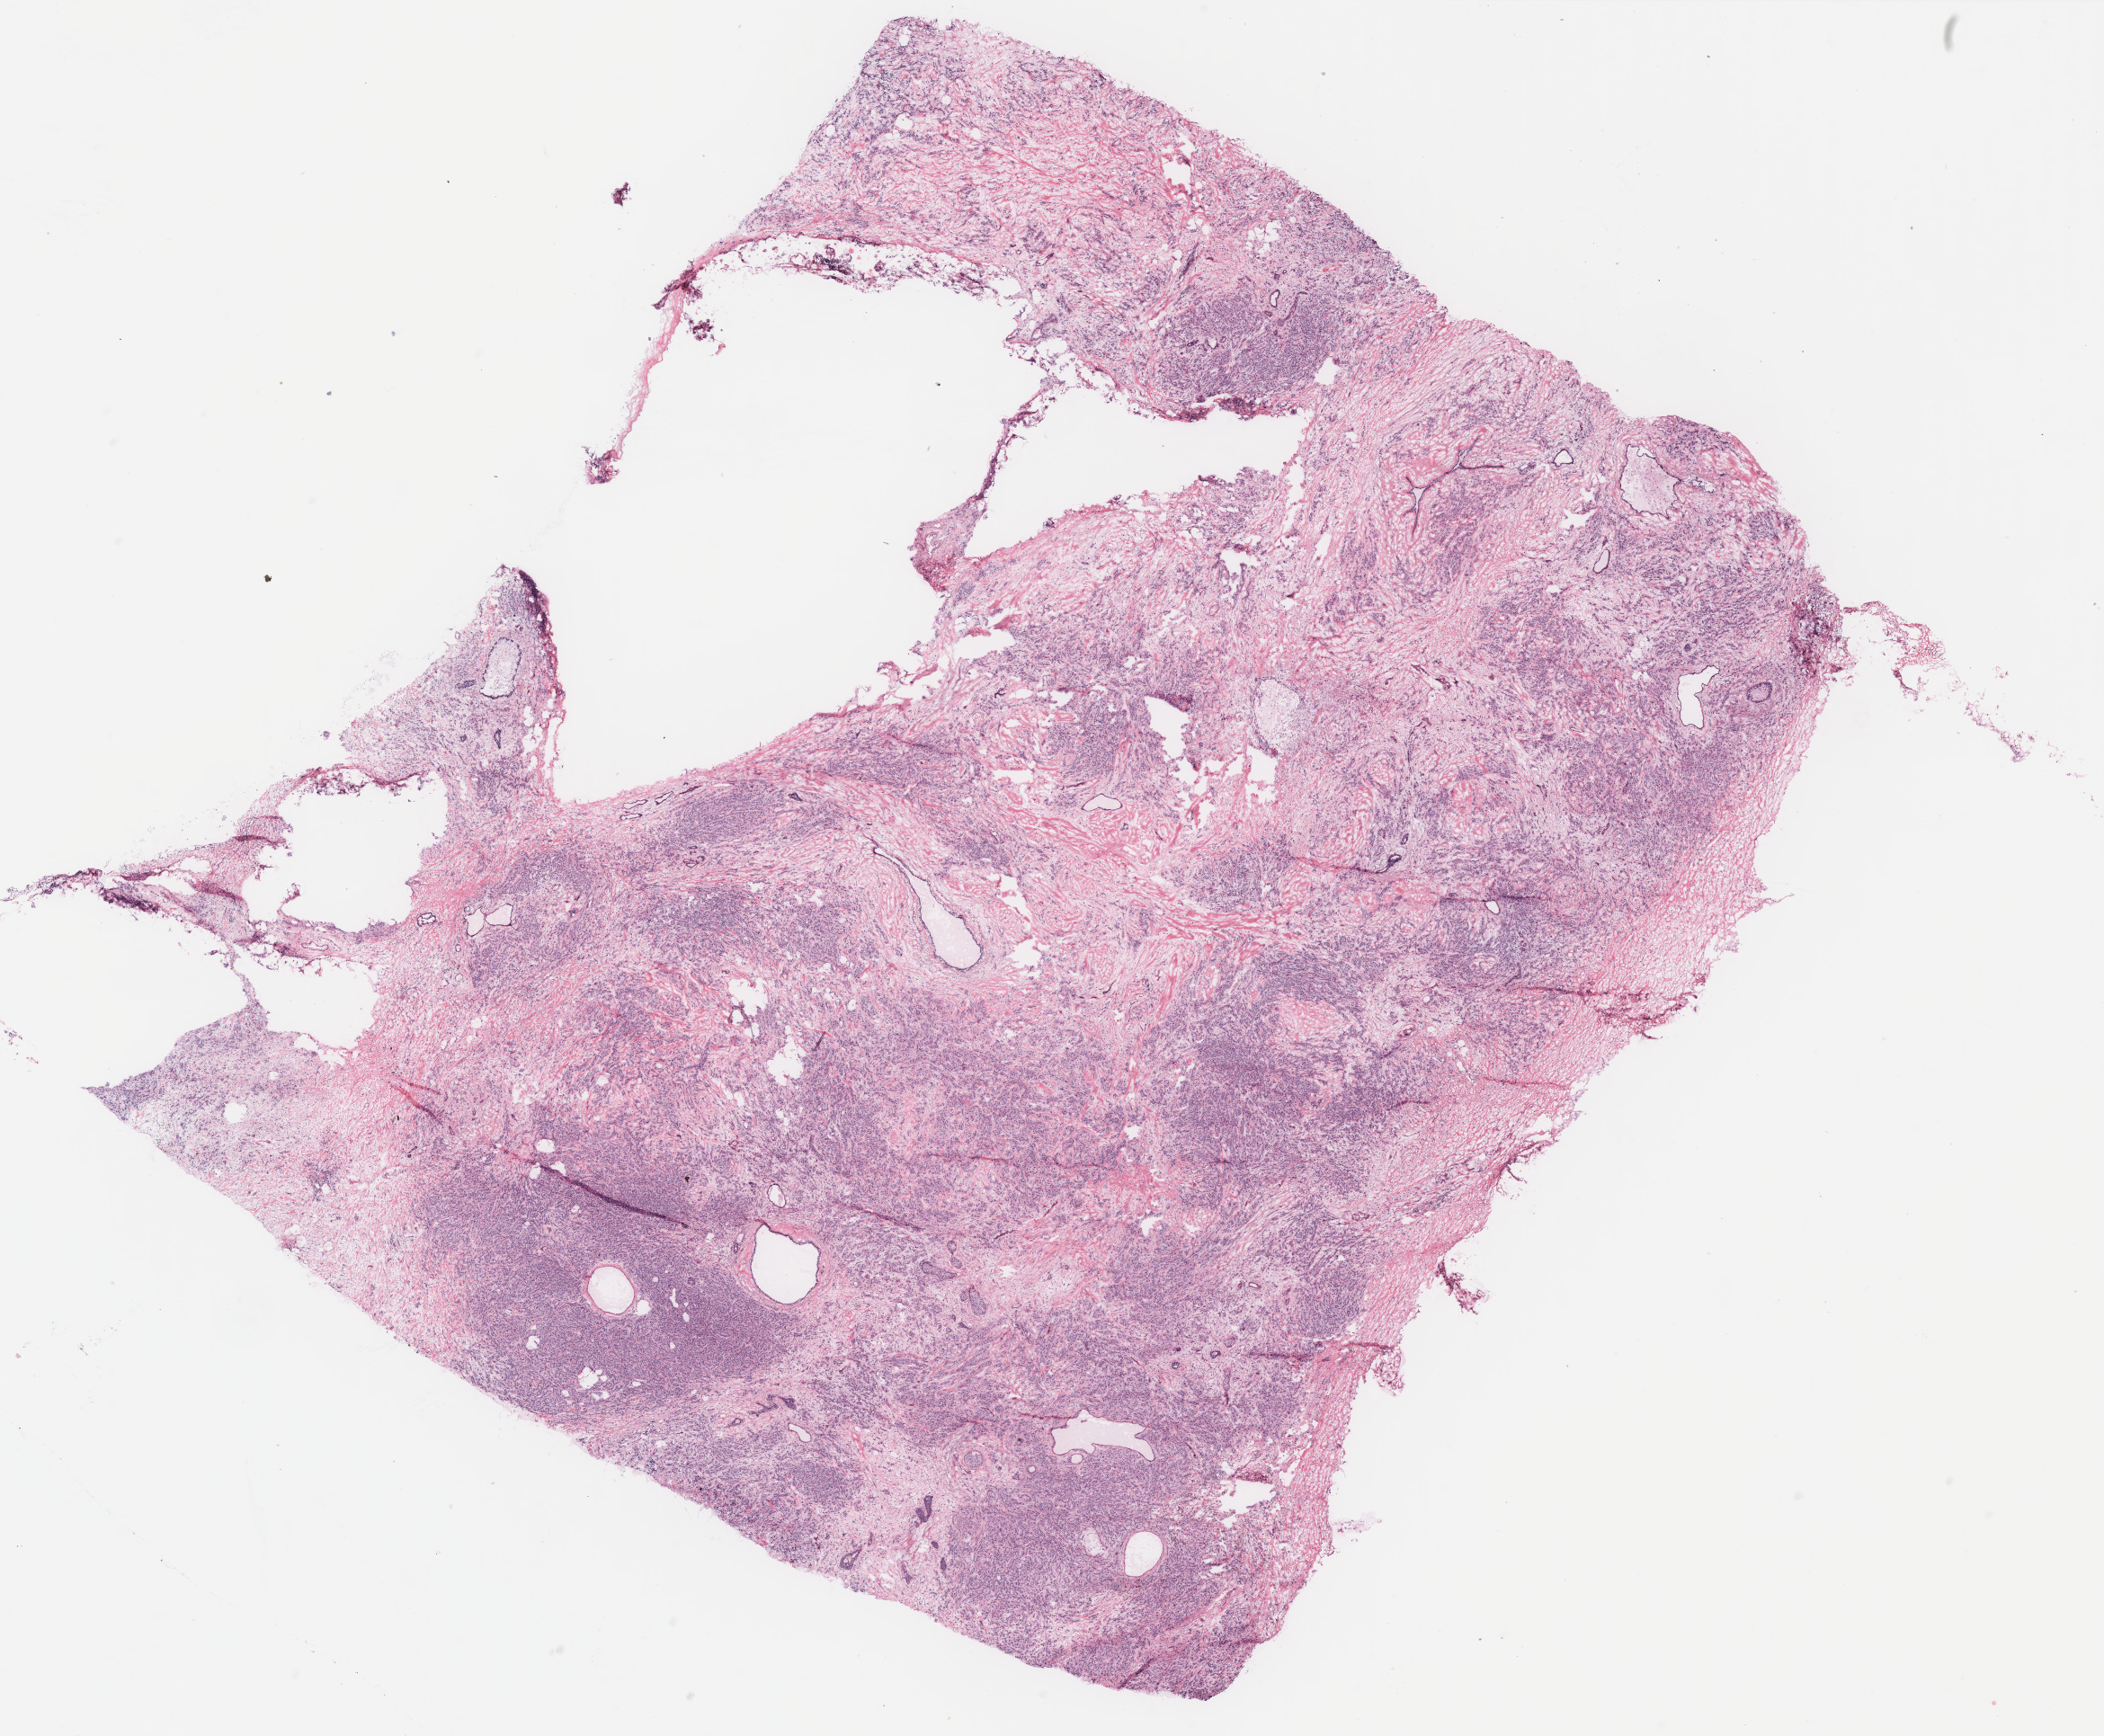
H&E whole-slide image — a low-resolution overview of the entire scanned area, about 18.7 x 15.5 mm; breast, tissue type not recorded. Female, 79 y/o.
Patient diagnosis: Infiltrating duct carcinoma, NOS.